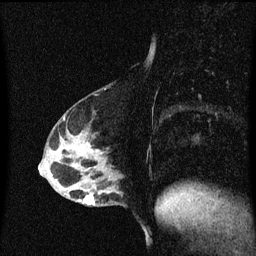
Breast MRI (dynamic contrast-enhanced), one sagittal slice; position 21 of 60 along the scan axis; dynamic contrast-enhanced series, image 2 of 3 at this slice position (ordered by acquisition); 1.5 T; TE 4.2 ms, TR 8.4 ms; 256 × 256 image matrix, field of view 200 × 200 mm. Female patient, age 40 years.
Structures marked on this image (semi-automatically segmented with operator editing):
- analysis volume of interest (the breast-tissue region the enhancement analysis was run in; not a lesion): bounding box [x1, y1, x2, y2] px = [82, 172, 125, 207]
- tumour enhancement mask (voxels above the 70 % enhancement threshold inside the analysis volume of interest): [85, 196, 96, 205]